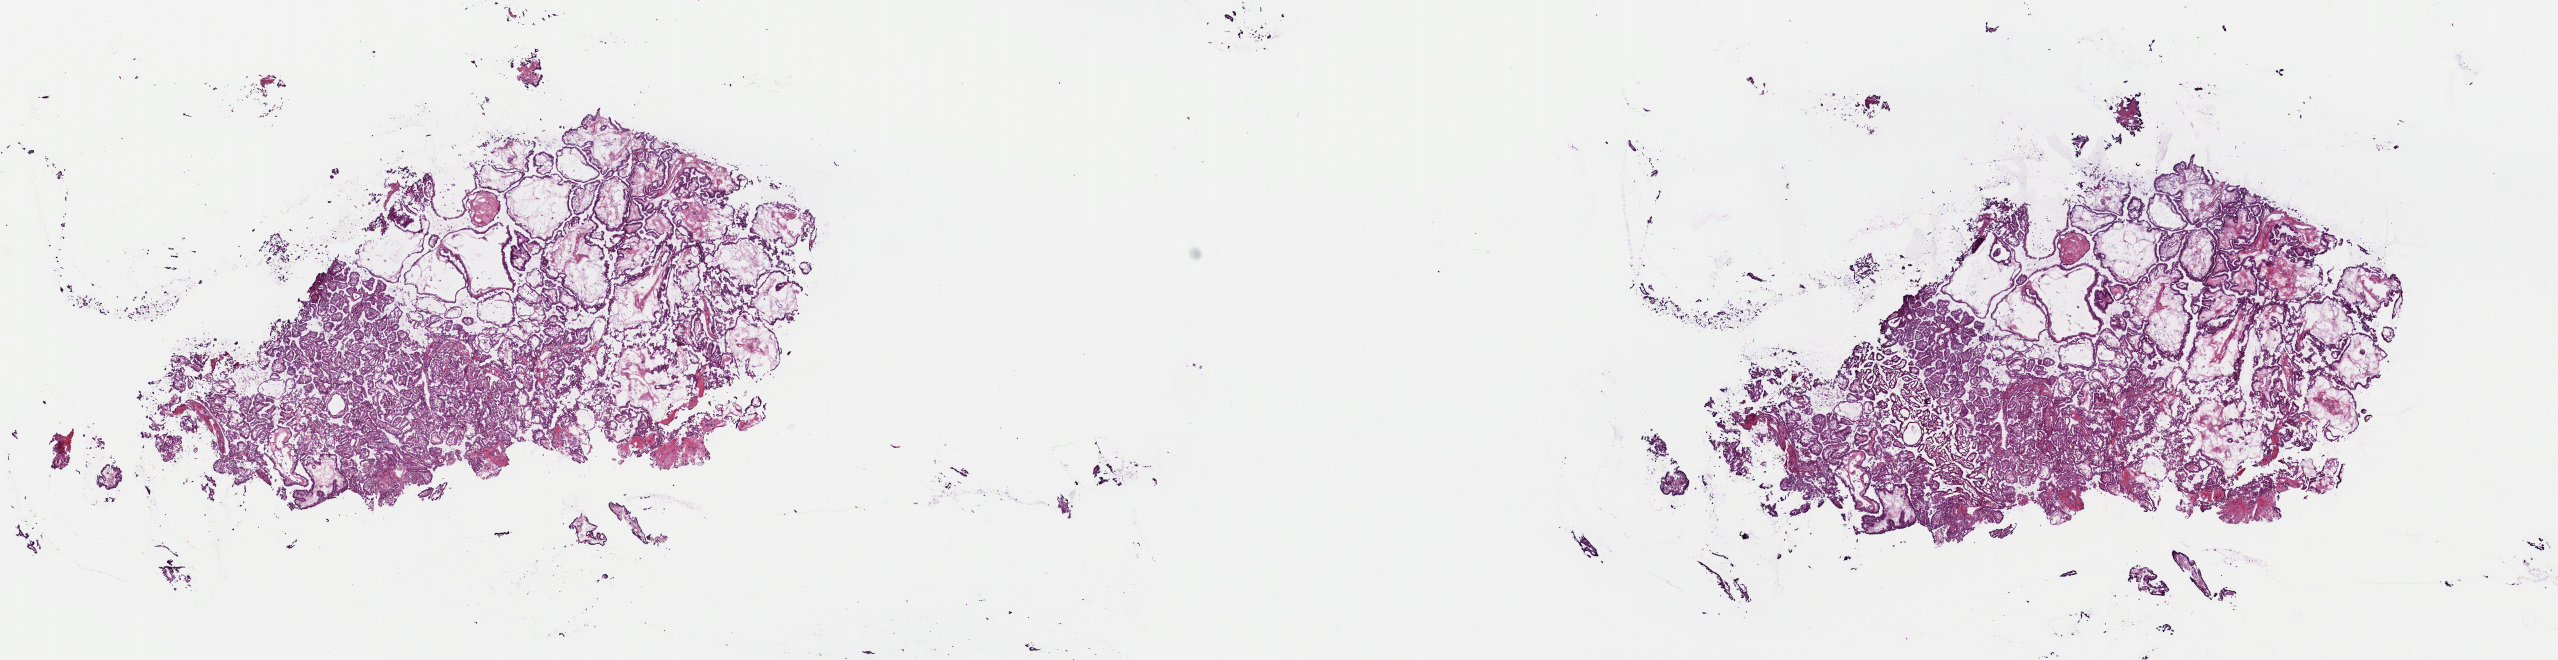
Whole-slide histology image, H&E — whole scanned area (about 20.2 x 5.2 mm) shown as a low-resolution overview. Frozen section from the top of the tissue portion. Thyroid, primary tumour sample. Female patient; age at initial diagnosis 32 years. Slide review estimates, as recorded: tumour cells 100%, tumour nuclei 92%, normal cells 0%, stromal cells 0%, necrosis 0%. Inflammatory infiltration, as recorded: lymphocyte infiltration 0%, monocyte infiltration 0%, neutrophil infiltration 0%.
Pathologic diagnosis: Papillary adenocarcinoma, NOS (thyroid gland). AJCC pathologic stage: I (7th edition). Laterality: left.